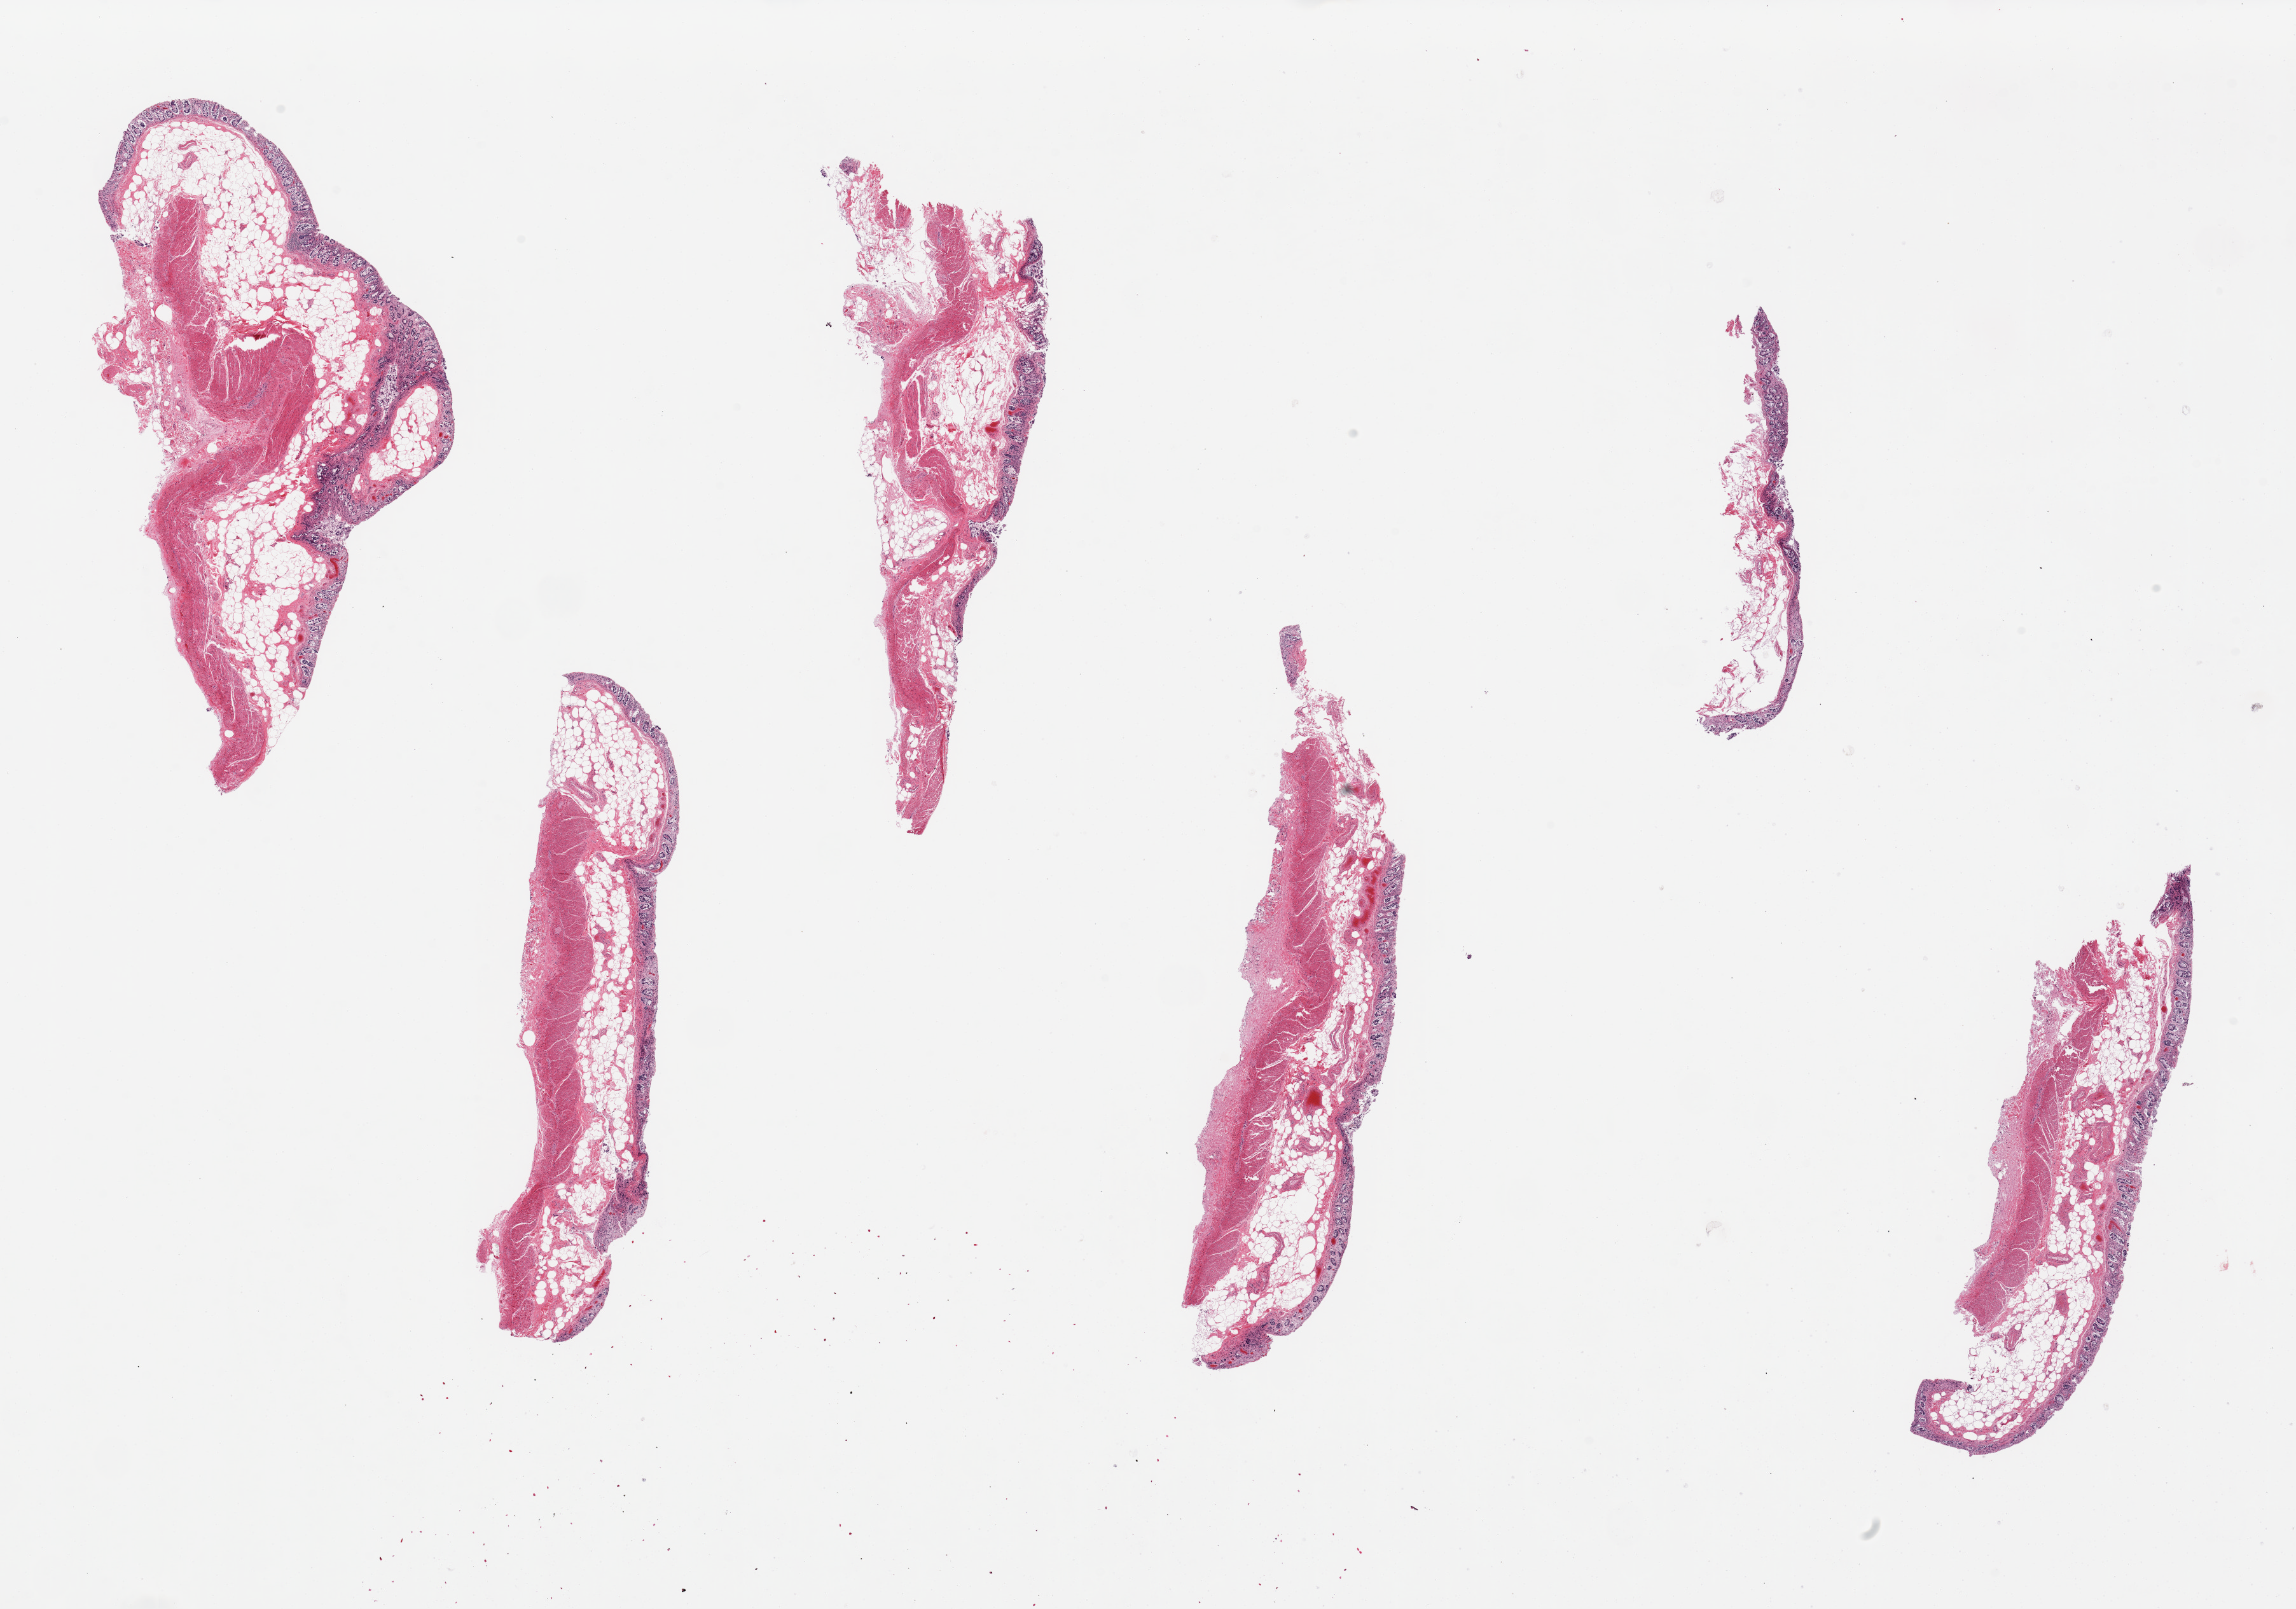
Digitized hematoxylin and eosin (H&E)-stained section, brightfield, whole scanned area (about 28.5 x 20.0 mm) shown as a low-resolution overview, PAXgene-fixed paraffin-embedded (PFPE) section, target tissue: transverse colon, tissue donor sample. Donor sex: male.
Pathologist's review note for this sample: 6 pieces, up to 9x2mm; mucosa sloughed.